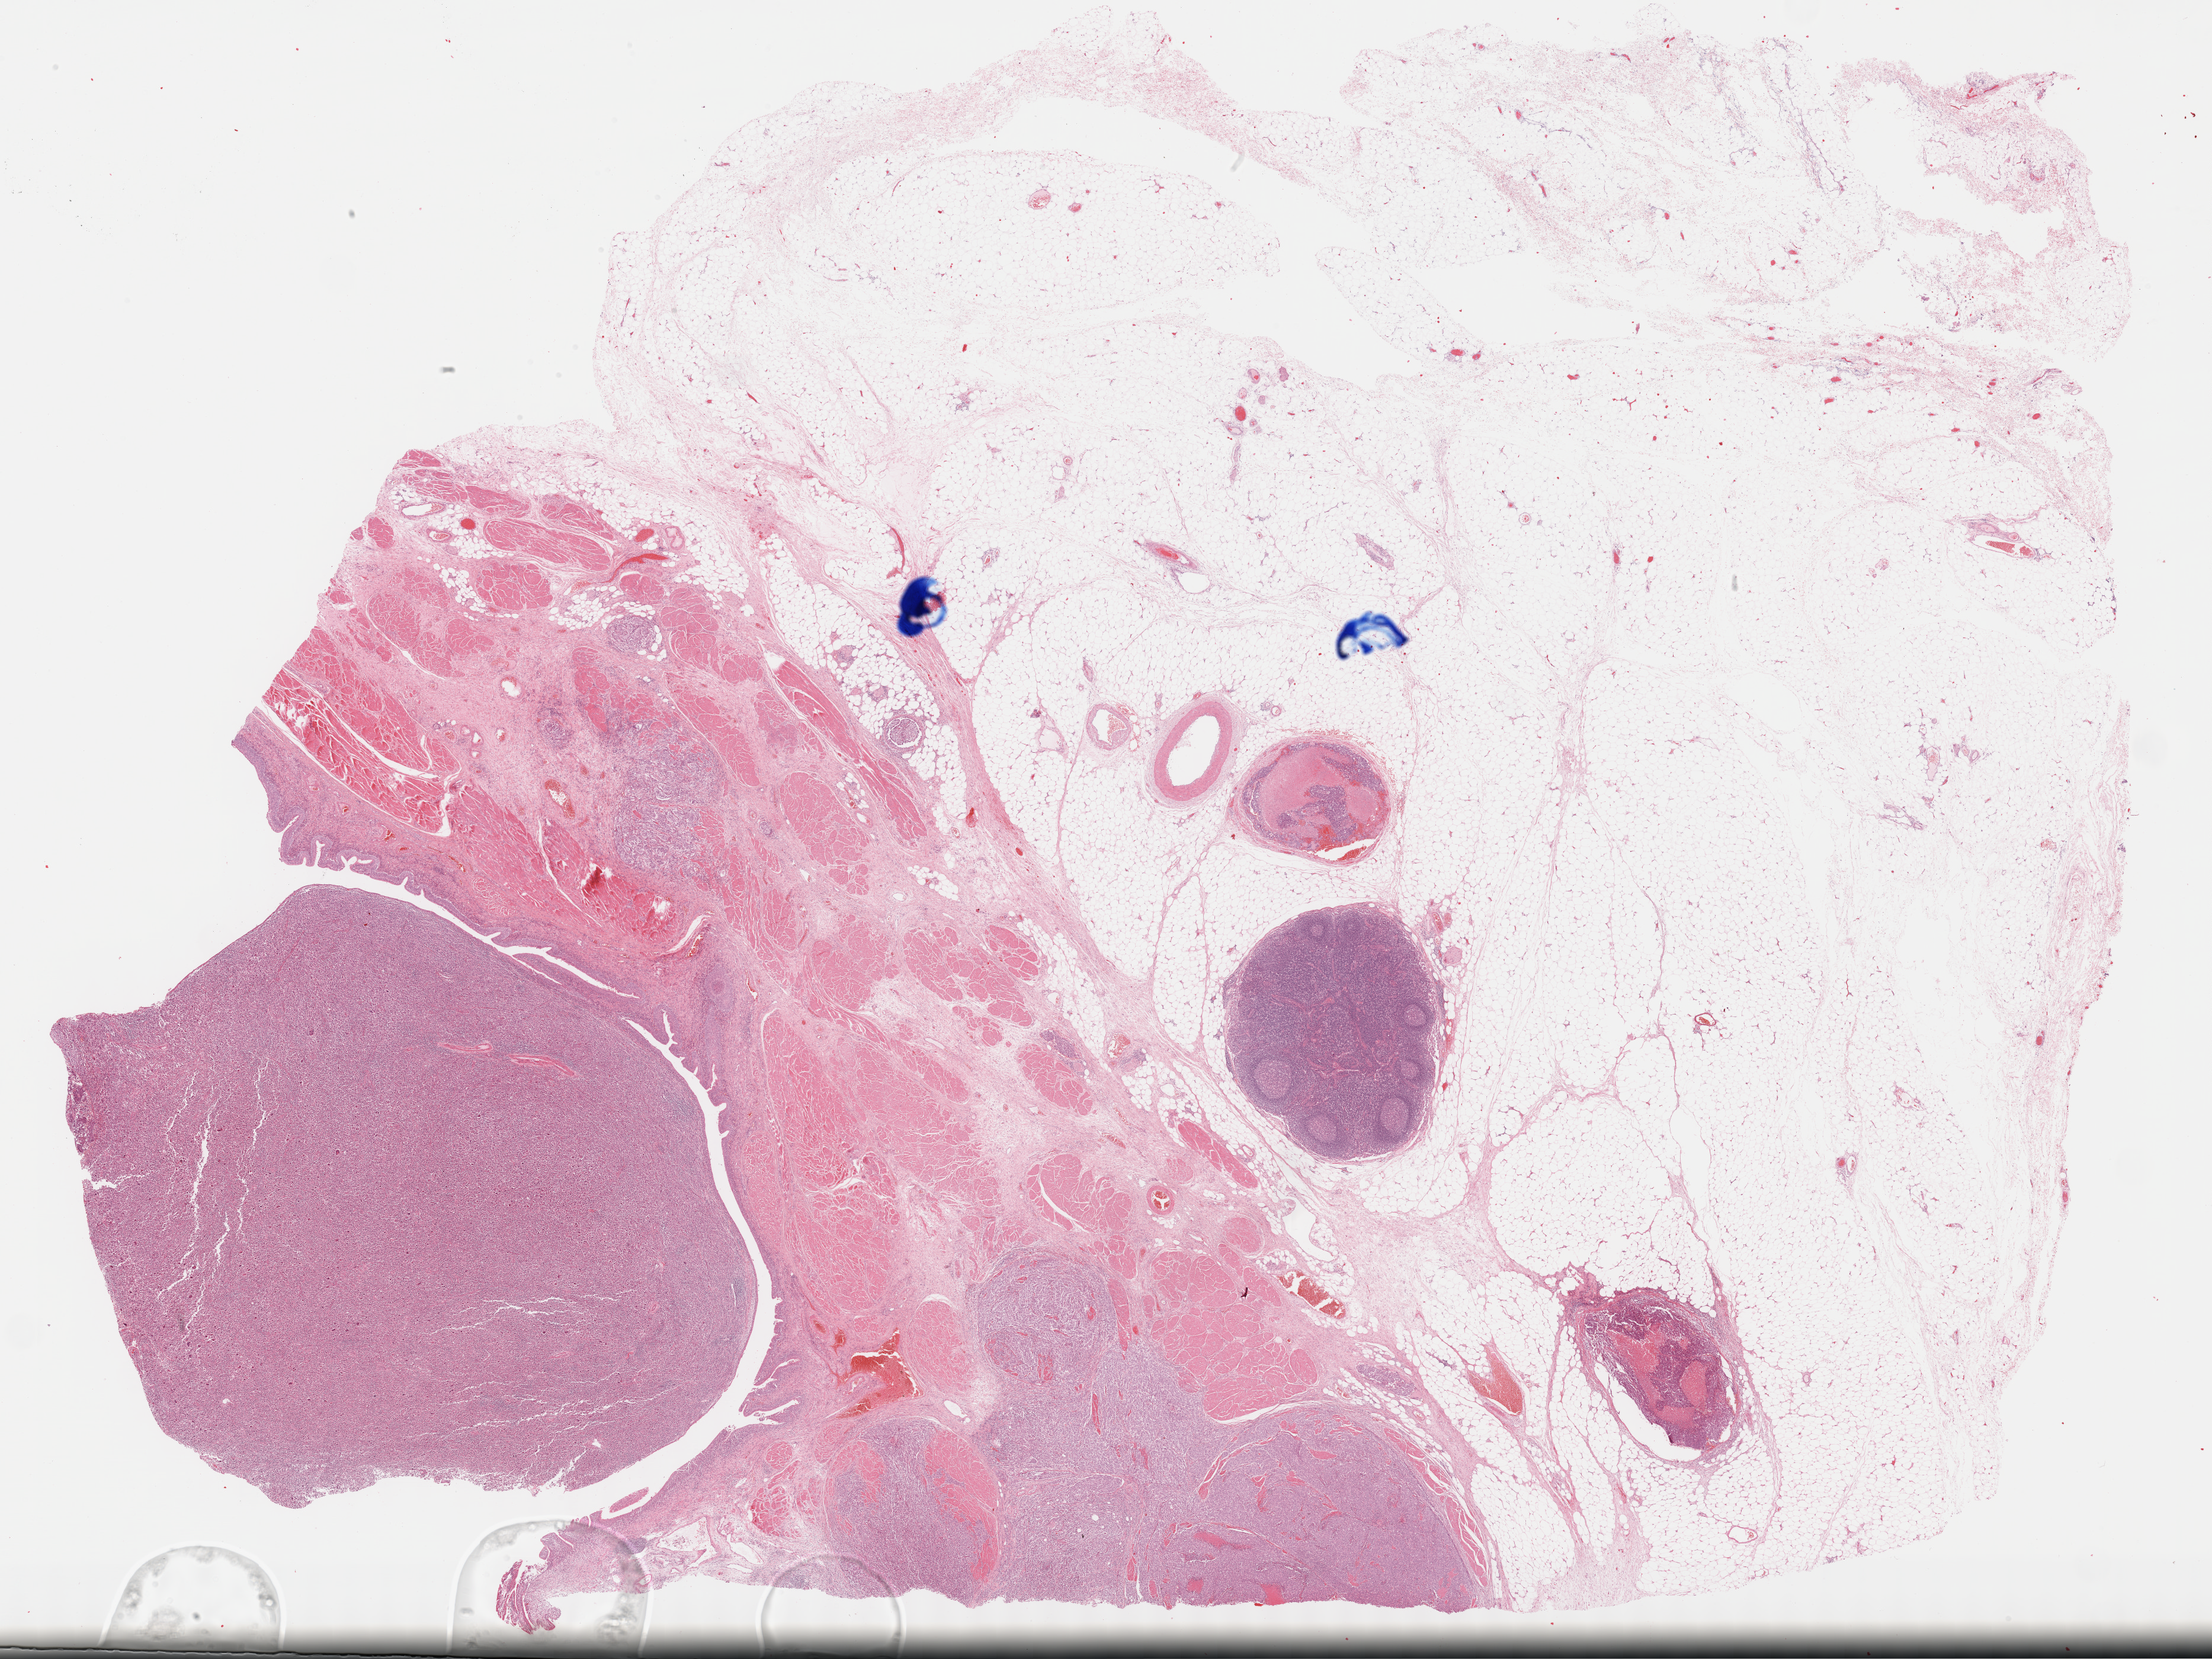
Whole-slide histology image, Hematoxylin and eosin (H&E) stained — whole scanned area (about 30.2 x 22.7 mm) shown as a low-resolution overview. Formalin-fixed paraffin-embedded (FFPE) diagnostic section. Primary tumour sample from the bladder. Female patient; age at initial diagnosis 67 years. Histologic grade: high grade.
Diagnosis: Transitional cell carcinoma. TNM: T3b NX M0. AJCC pathologic stage: III (7th edition).